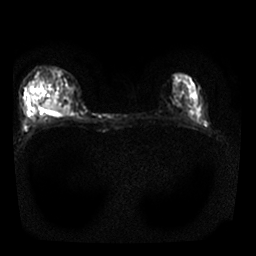
Breast MRI, one axial slice; slice 12 of 25 in the series (ordered by position); diffusion-weighted series; image 2 of 4 stored at this slice position (different b-values; order by instance number); 1.5 T; 4 mm slice thickness; 256 × 256 image matrix, field of view 310 × 310 mm. Female patient.
Structures marked on this image (expert manual segmentation):
- tumour on diffusion-weighted imaging: box from (x=41, y=102) to (x=62, y=113) px